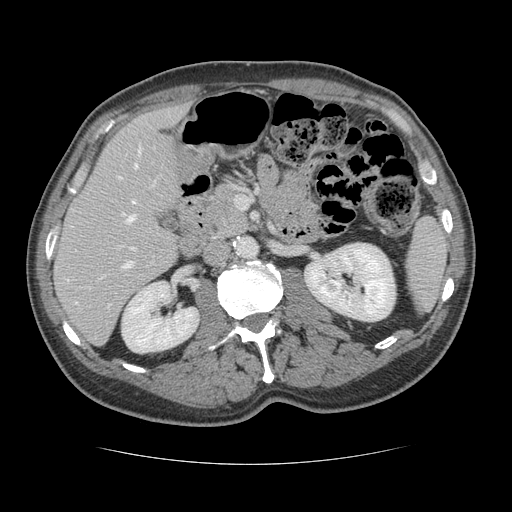
Contrast-enhanced abdominal CT, one axial slice. Position 64 of 134 along the scan axis. Reconstruction kernel STANDARD. Intravenous contrast given. Soft-tissue window (W 400 / L 40 HU). 2.5 mm slice thickness. 512 × 512 image matrix, field of view 377 × 377 mm. Male patient, age 68 years. Case-level facts recorded for this patient, not image findings: diagnosis: colorectal cancer liver metastases, imaged before liver resection; multiple liver metastases: yes; largest metastasis: 2.2 cm; disease in both lobes: no.
Outlined on this slice (manually delineated by an expert):
- hepatic veins: bounding box [x1, y1, x2, y2] px = [75, 147, 141, 304]
- liver: [55, 108, 184, 343]
- planned liver remnant (the part of the liver to remain after resection): [56, 107, 184, 335]
- portal vein (with intrahepatic branches): [122, 213, 134, 268]